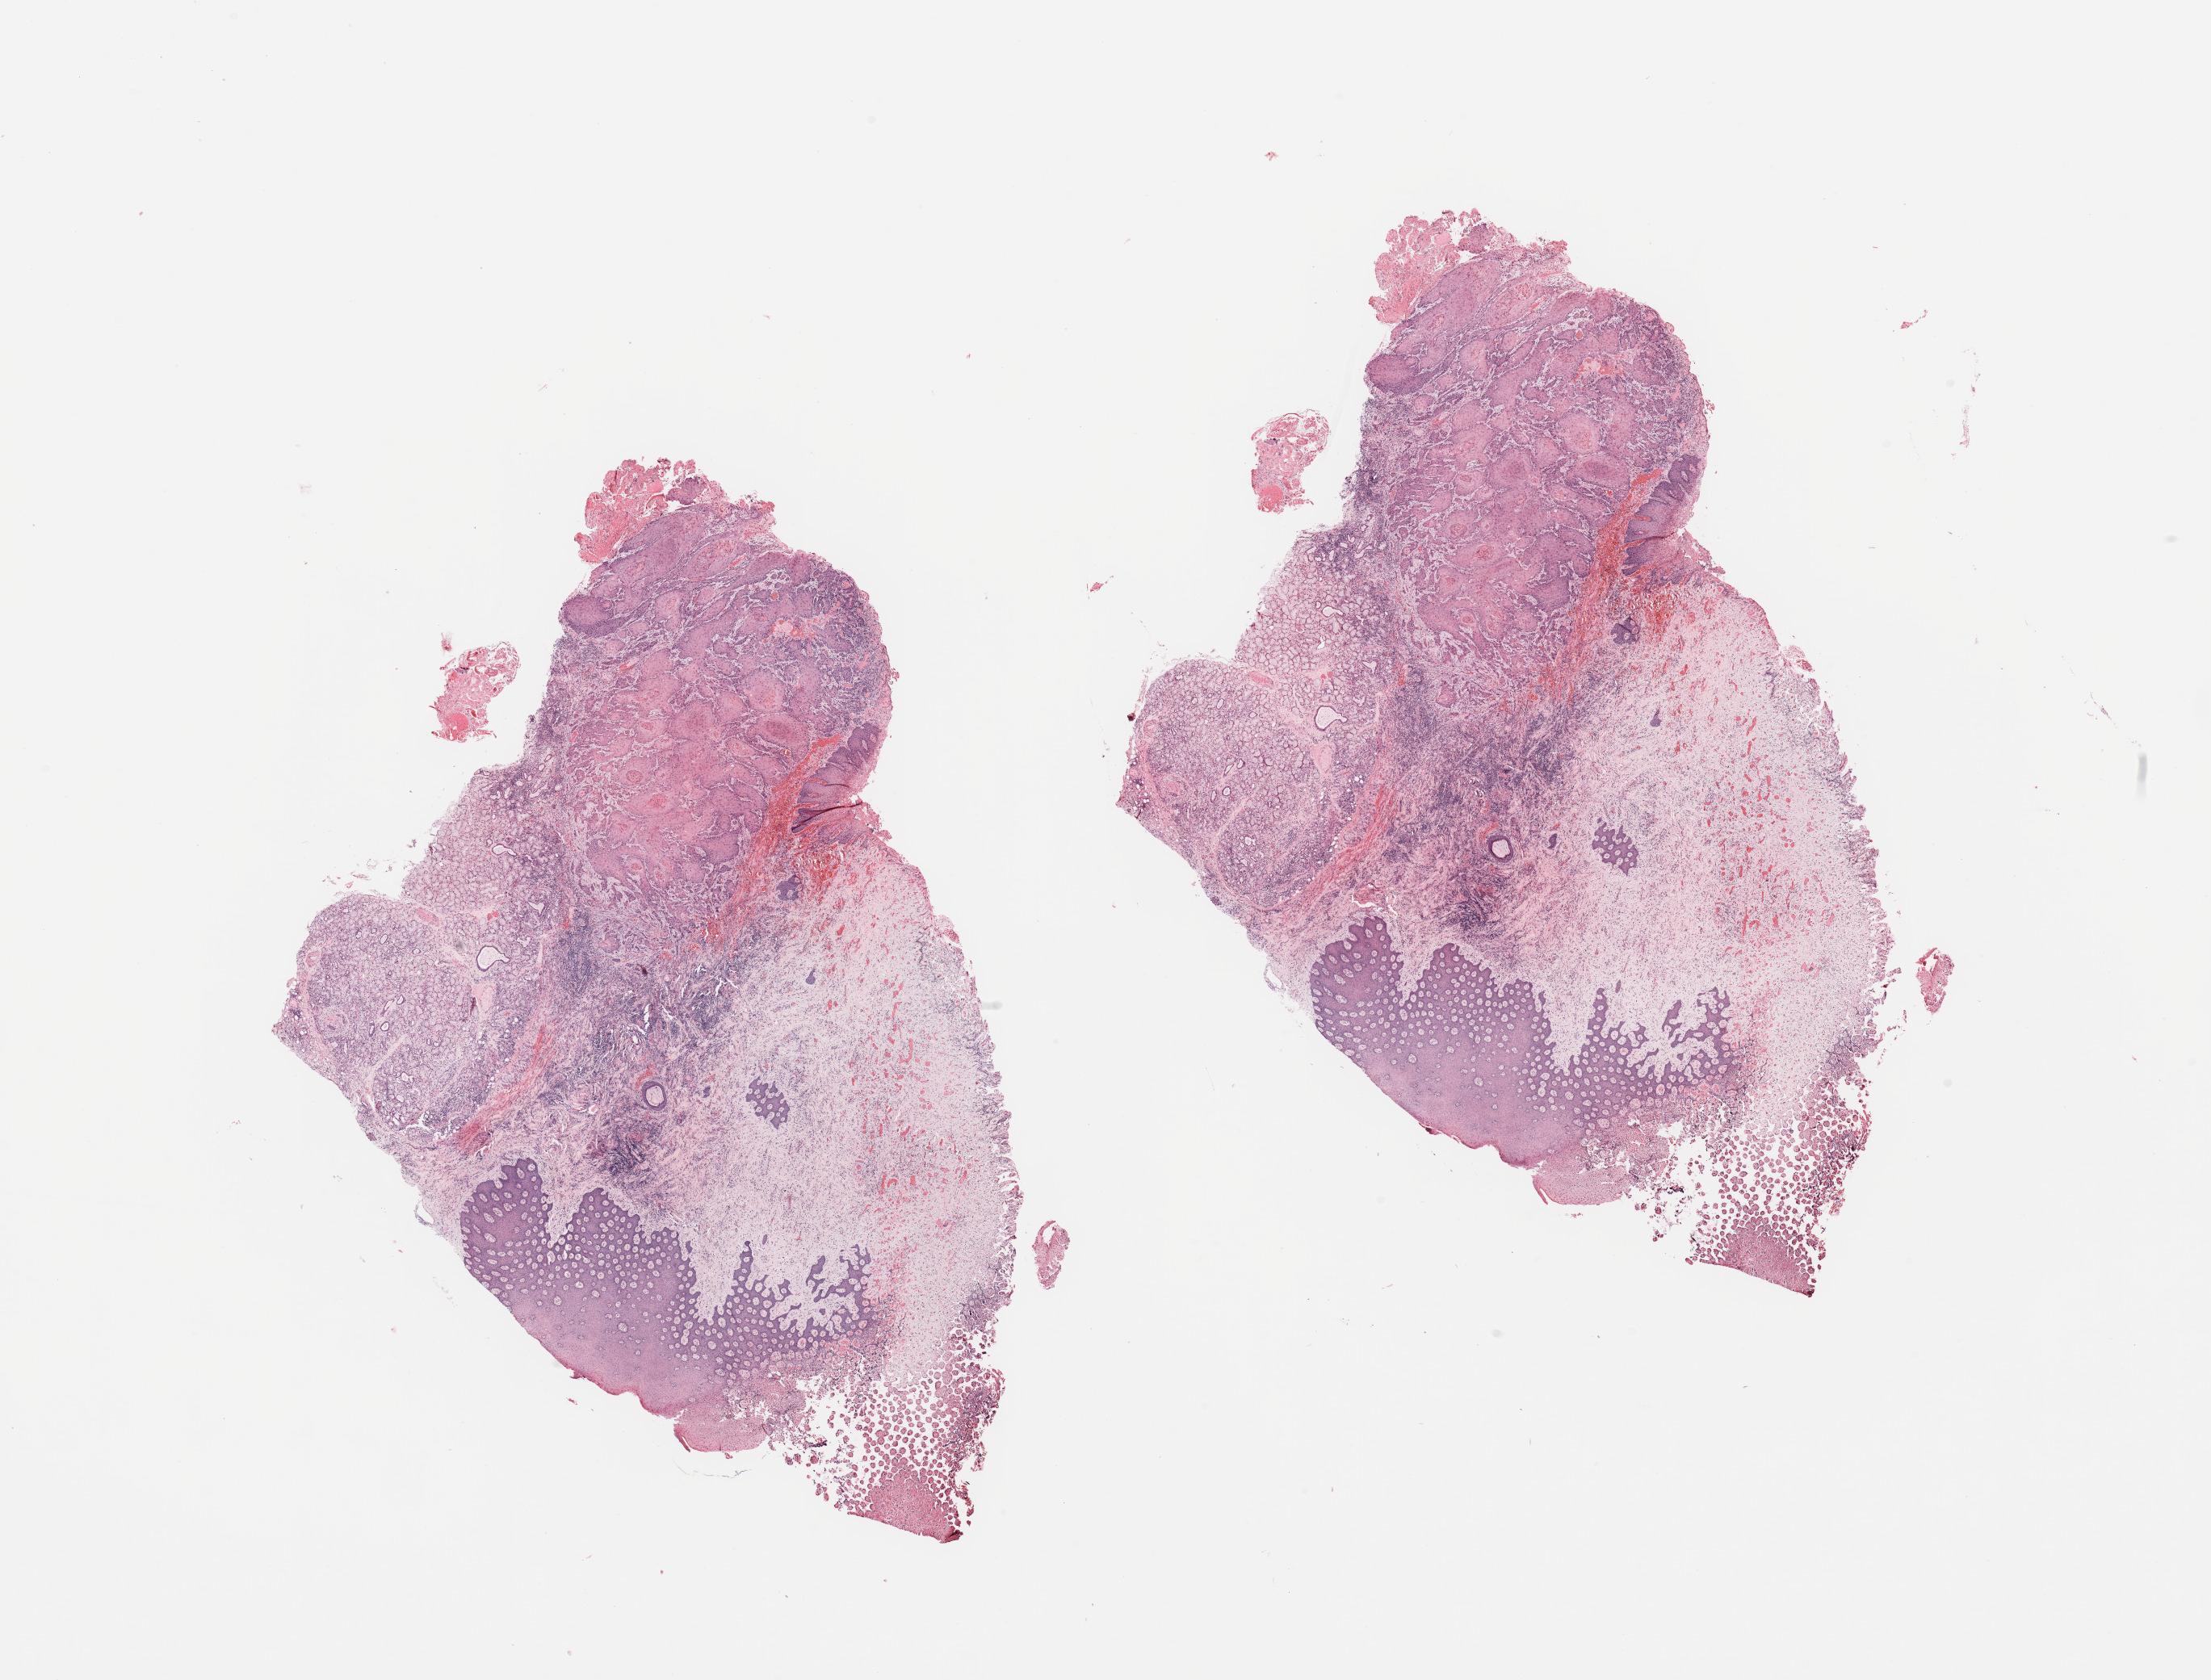
H&E-stained whole-slide image, whole scanned area (about 21.7 x 16.5 mm) shown as a low-resolution overview. Normal (non-tumour) tissue sample, head and neck. Patient: female, age 67 years.
This section: normal (non-tumour) tissue from the same patient. Patient diagnosis: Squamous cell carcinoma, NOS (overlapping lesion of lip, oral cavity and pharynx).